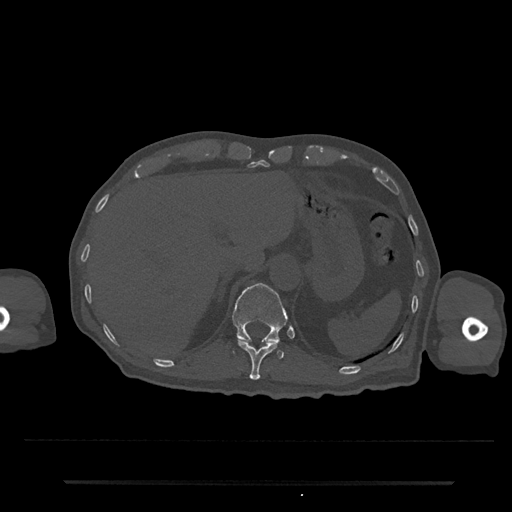
CT including the spine, one axial slice; position 226 of 797 along the scan axis; 120 kVp; bone window (W 1800 / L 400 HU); 512 × 512 image matrix, field of view 427 × 427 mm. Patient: male, 74 years. From the clinical record (not read from this slice): primary cancer: prostate.
Annotated regions visible in this slice (semi-automatically segmented with operator editing):
- T11 vertebra: box from (x=237, y=339) to (x=279, y=380) px
- T12 vertebra: (x=232, y=283)–(x=288, y=359)